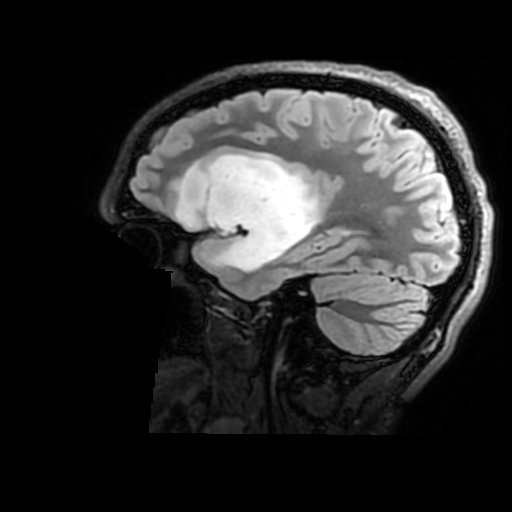
Brain MRI from a brain-tumour surgery series, one sagittal slice; position 121 of 176 along the scan axis; T2 FLAIR; 1 mm slice thickness; 512 × 512 image matrix, field of view 240 × 240 mm. Case-level facts recorded for this patient, not image findings: histopathology: Astrocytoma; WHO grade: 2; IDH mutation: yes; tumour location: Right Insular.
Structures marked on this image (expert manual segmentation):
- tumour: bounding box (x1, y1, x2, y2) in pixels: (177, 154, 322, 273)